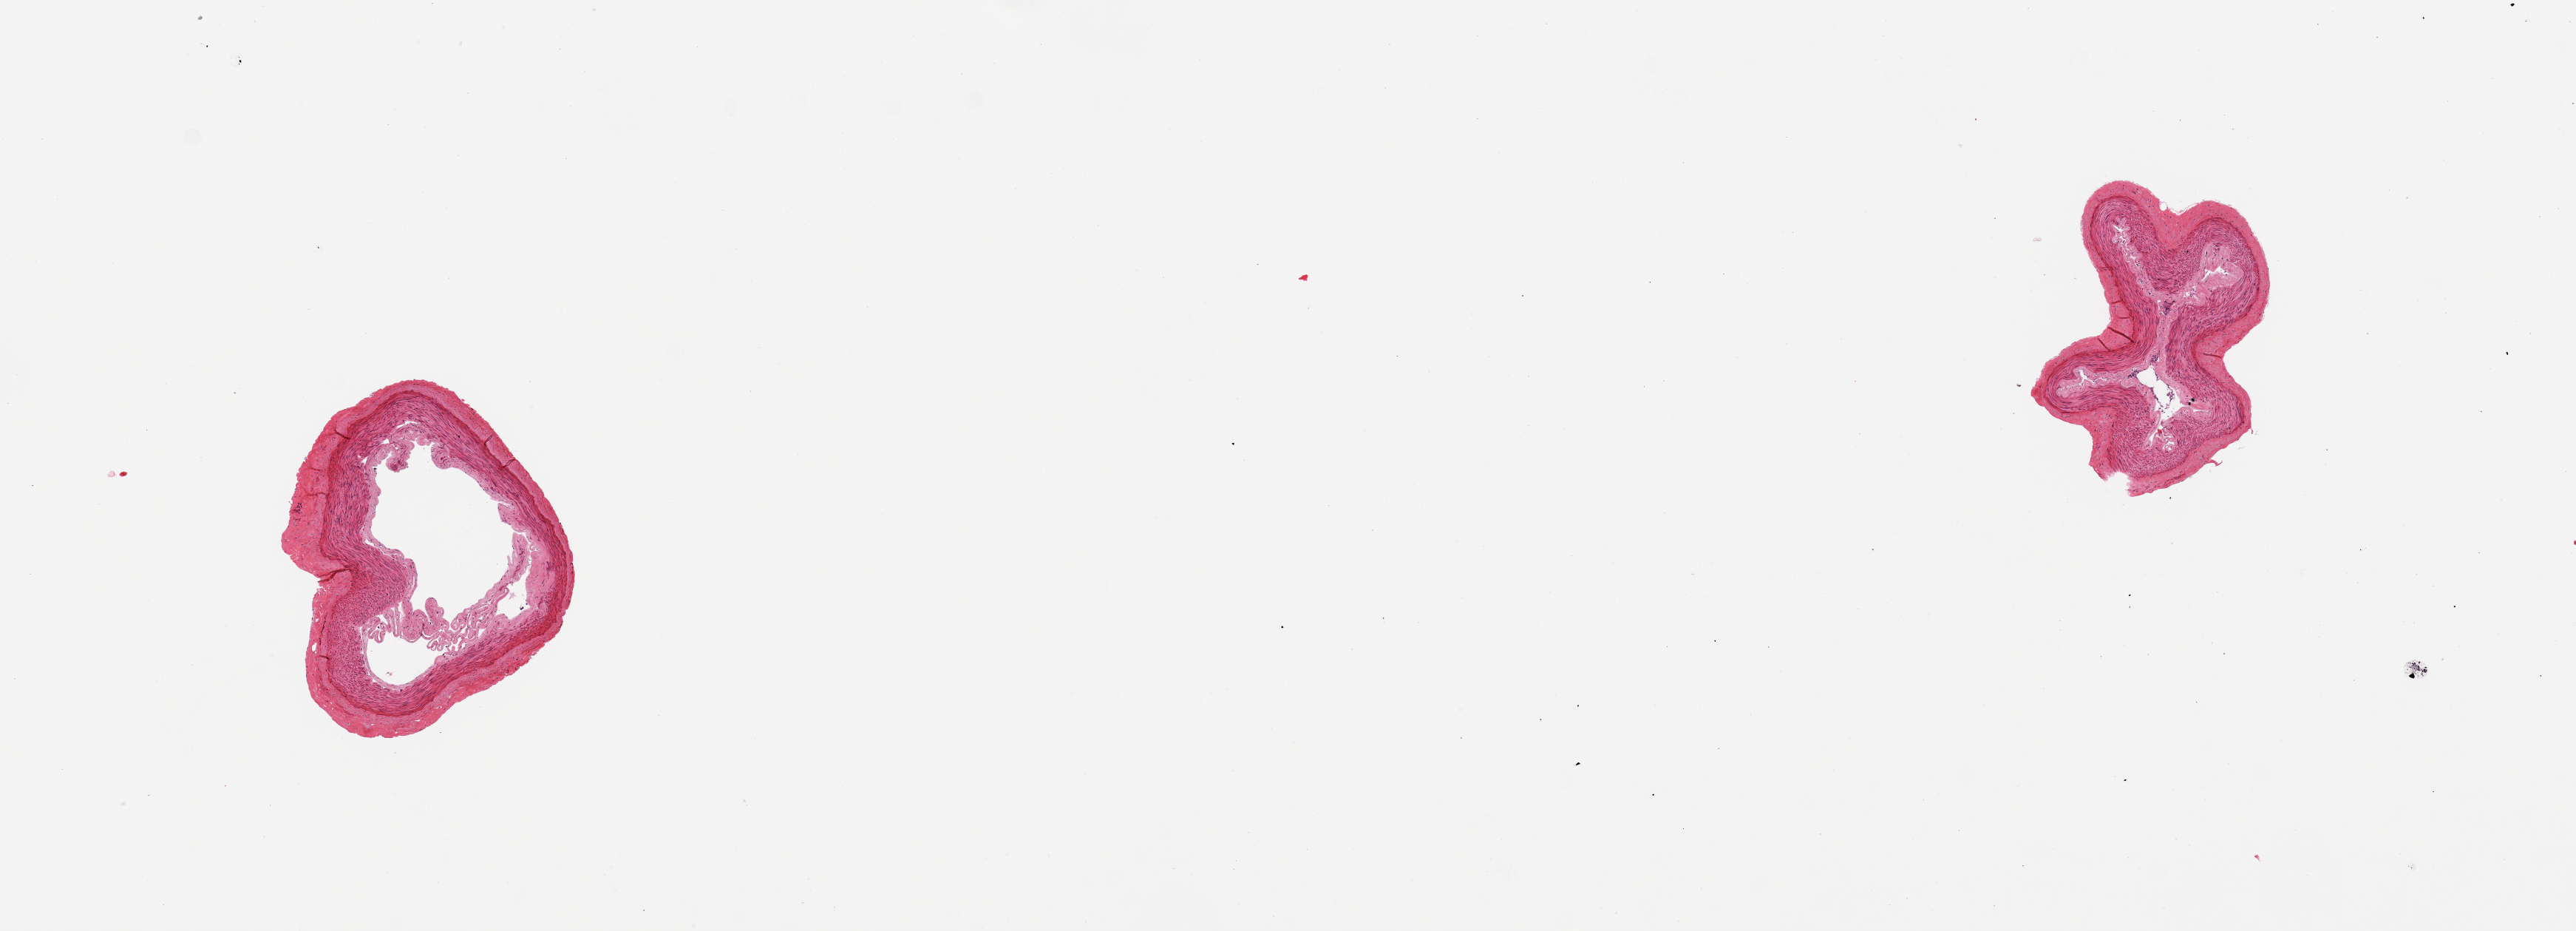
Hematoxylin and eosin (H&E) whole-slide image, a low-resolution overview of the entire scanned area, about 13.8 x 5.0 mm (acquisition: 20x scan), PAXgene-fixed, paraffin-embedded tissue, section of tibial artery (target tissue), donor tissue sample. Donor: female.
Review note (as recorded): 2 pieces, excellent clean specimens.